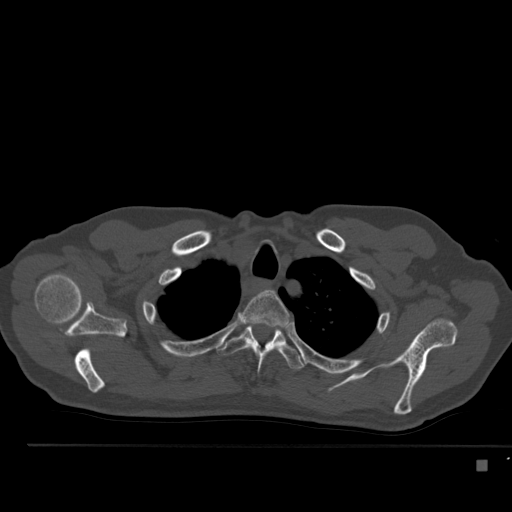
CT including the spine, one axial slice. Slice 404 of 517 in the series (ordered by position). Reconstruction kernel Br40s. Bone window (W 1800 / L 400 HU). 1.5 mm slice thickness. 512 × 512 image matrix, field of view 408 × 408 mm. Patient: male, 70 years. From the clinical record (not read from this slice): primary cancer: renal.
Annotated regions visible in this slice (semi-automatic segmentation, software-assisted and operator-edited):
- T2 vertebra: box from (x=240, y=290) to (x=290, y=328) px
- T3 vertebra: (x=217, y=323)–(x=306, y=375)